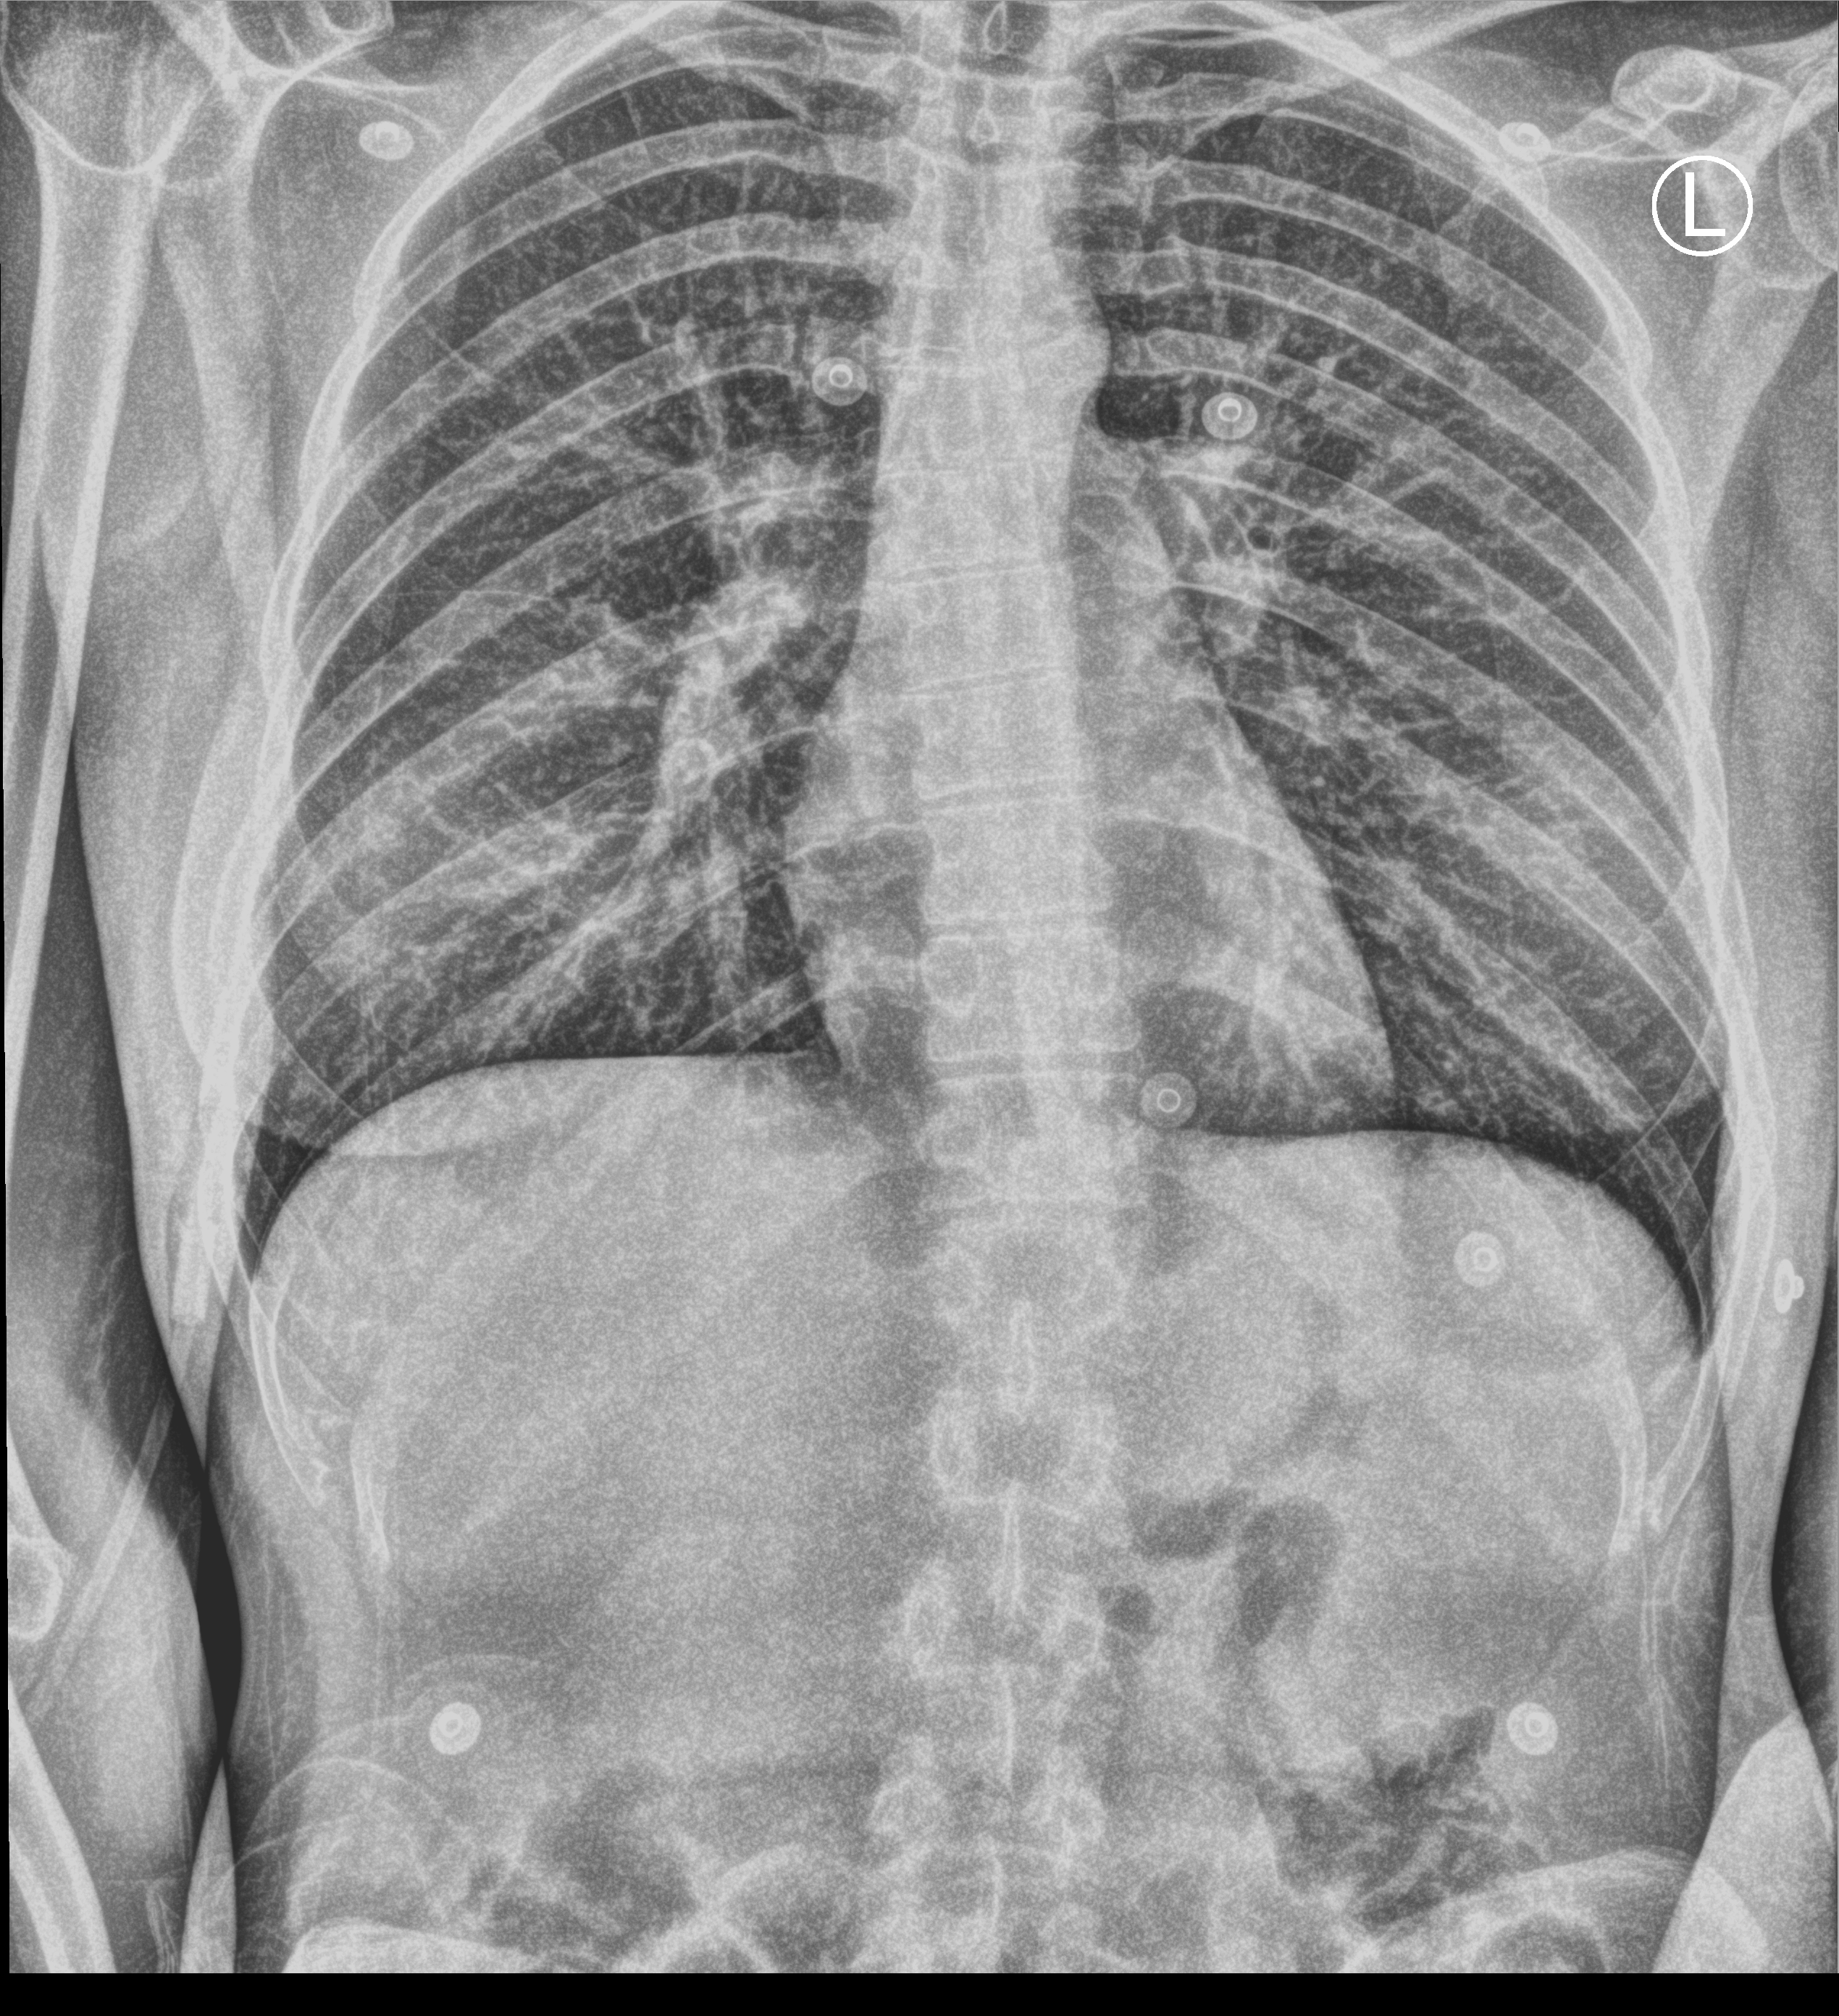
Portable chest radiograph, anteroposterior (AP) projection. Female patient hospitalised with COVID-19, age 18–59 years.
Admission-level facts for this patient (not findings on this image; timing relative to this image not recorded): admitted to intensive care during this hospital stay: no.